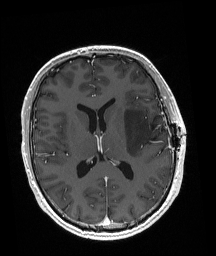
Brain MRI from a brain-tumour surgery series, one axial slice. Slice 90 of 192 in the series (ordered by position). T1-weighted post-contrast. 216 × 256 image matrix, field of view 211 × 250 mm. From the clinical record (not read from this slice): histopathology: Astrocytoma; WHO grade: 3; IDH mutation: yes.
Annotated regions visible in this slice (manually delineated by an expert):
- tumour: bounding box <124,109,160,157> (left, top, right, bottom; pixels)